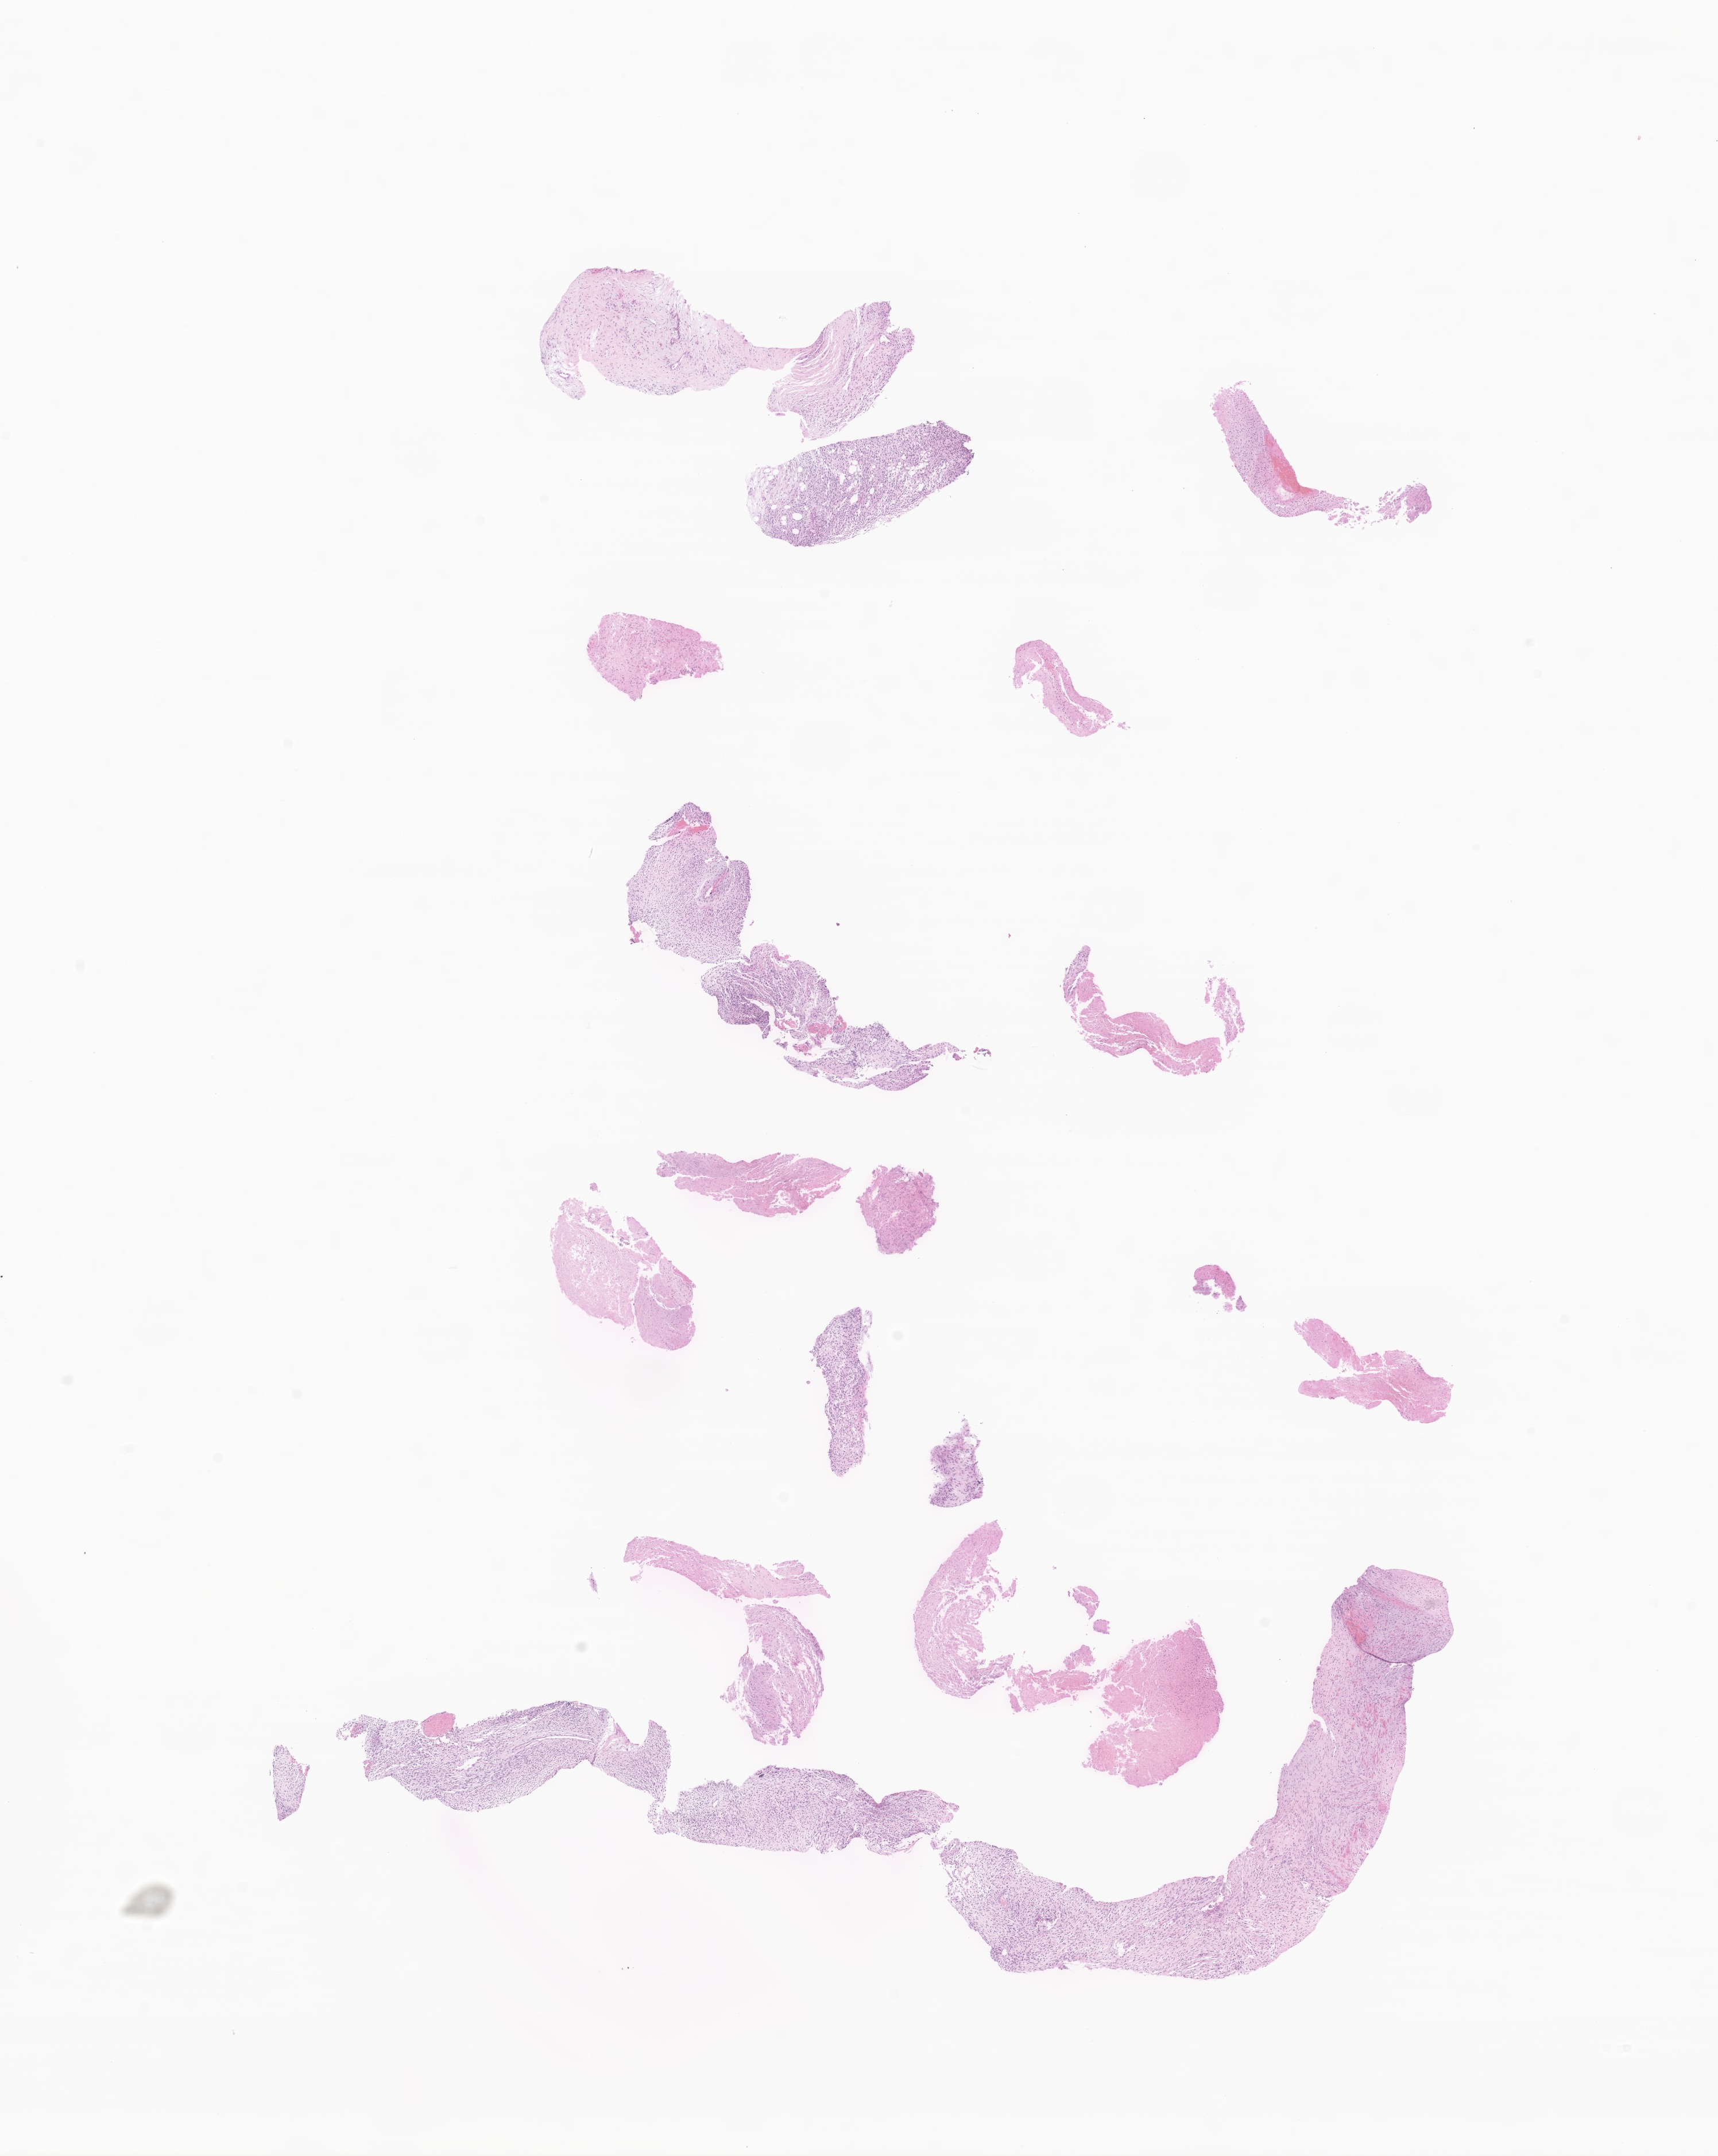
Digitized H&E-stained section of tumor tissue from the nerve of pelvis — a low-resolution overview of the entire scanned area, about 12.6 x 15.8 mm, formalin-fixed paraffin-embedded section. Female patient, age 241 months (20 years 1 month).
Diagnosis: Malignant peripheral nerve sheath tumor, NOS.